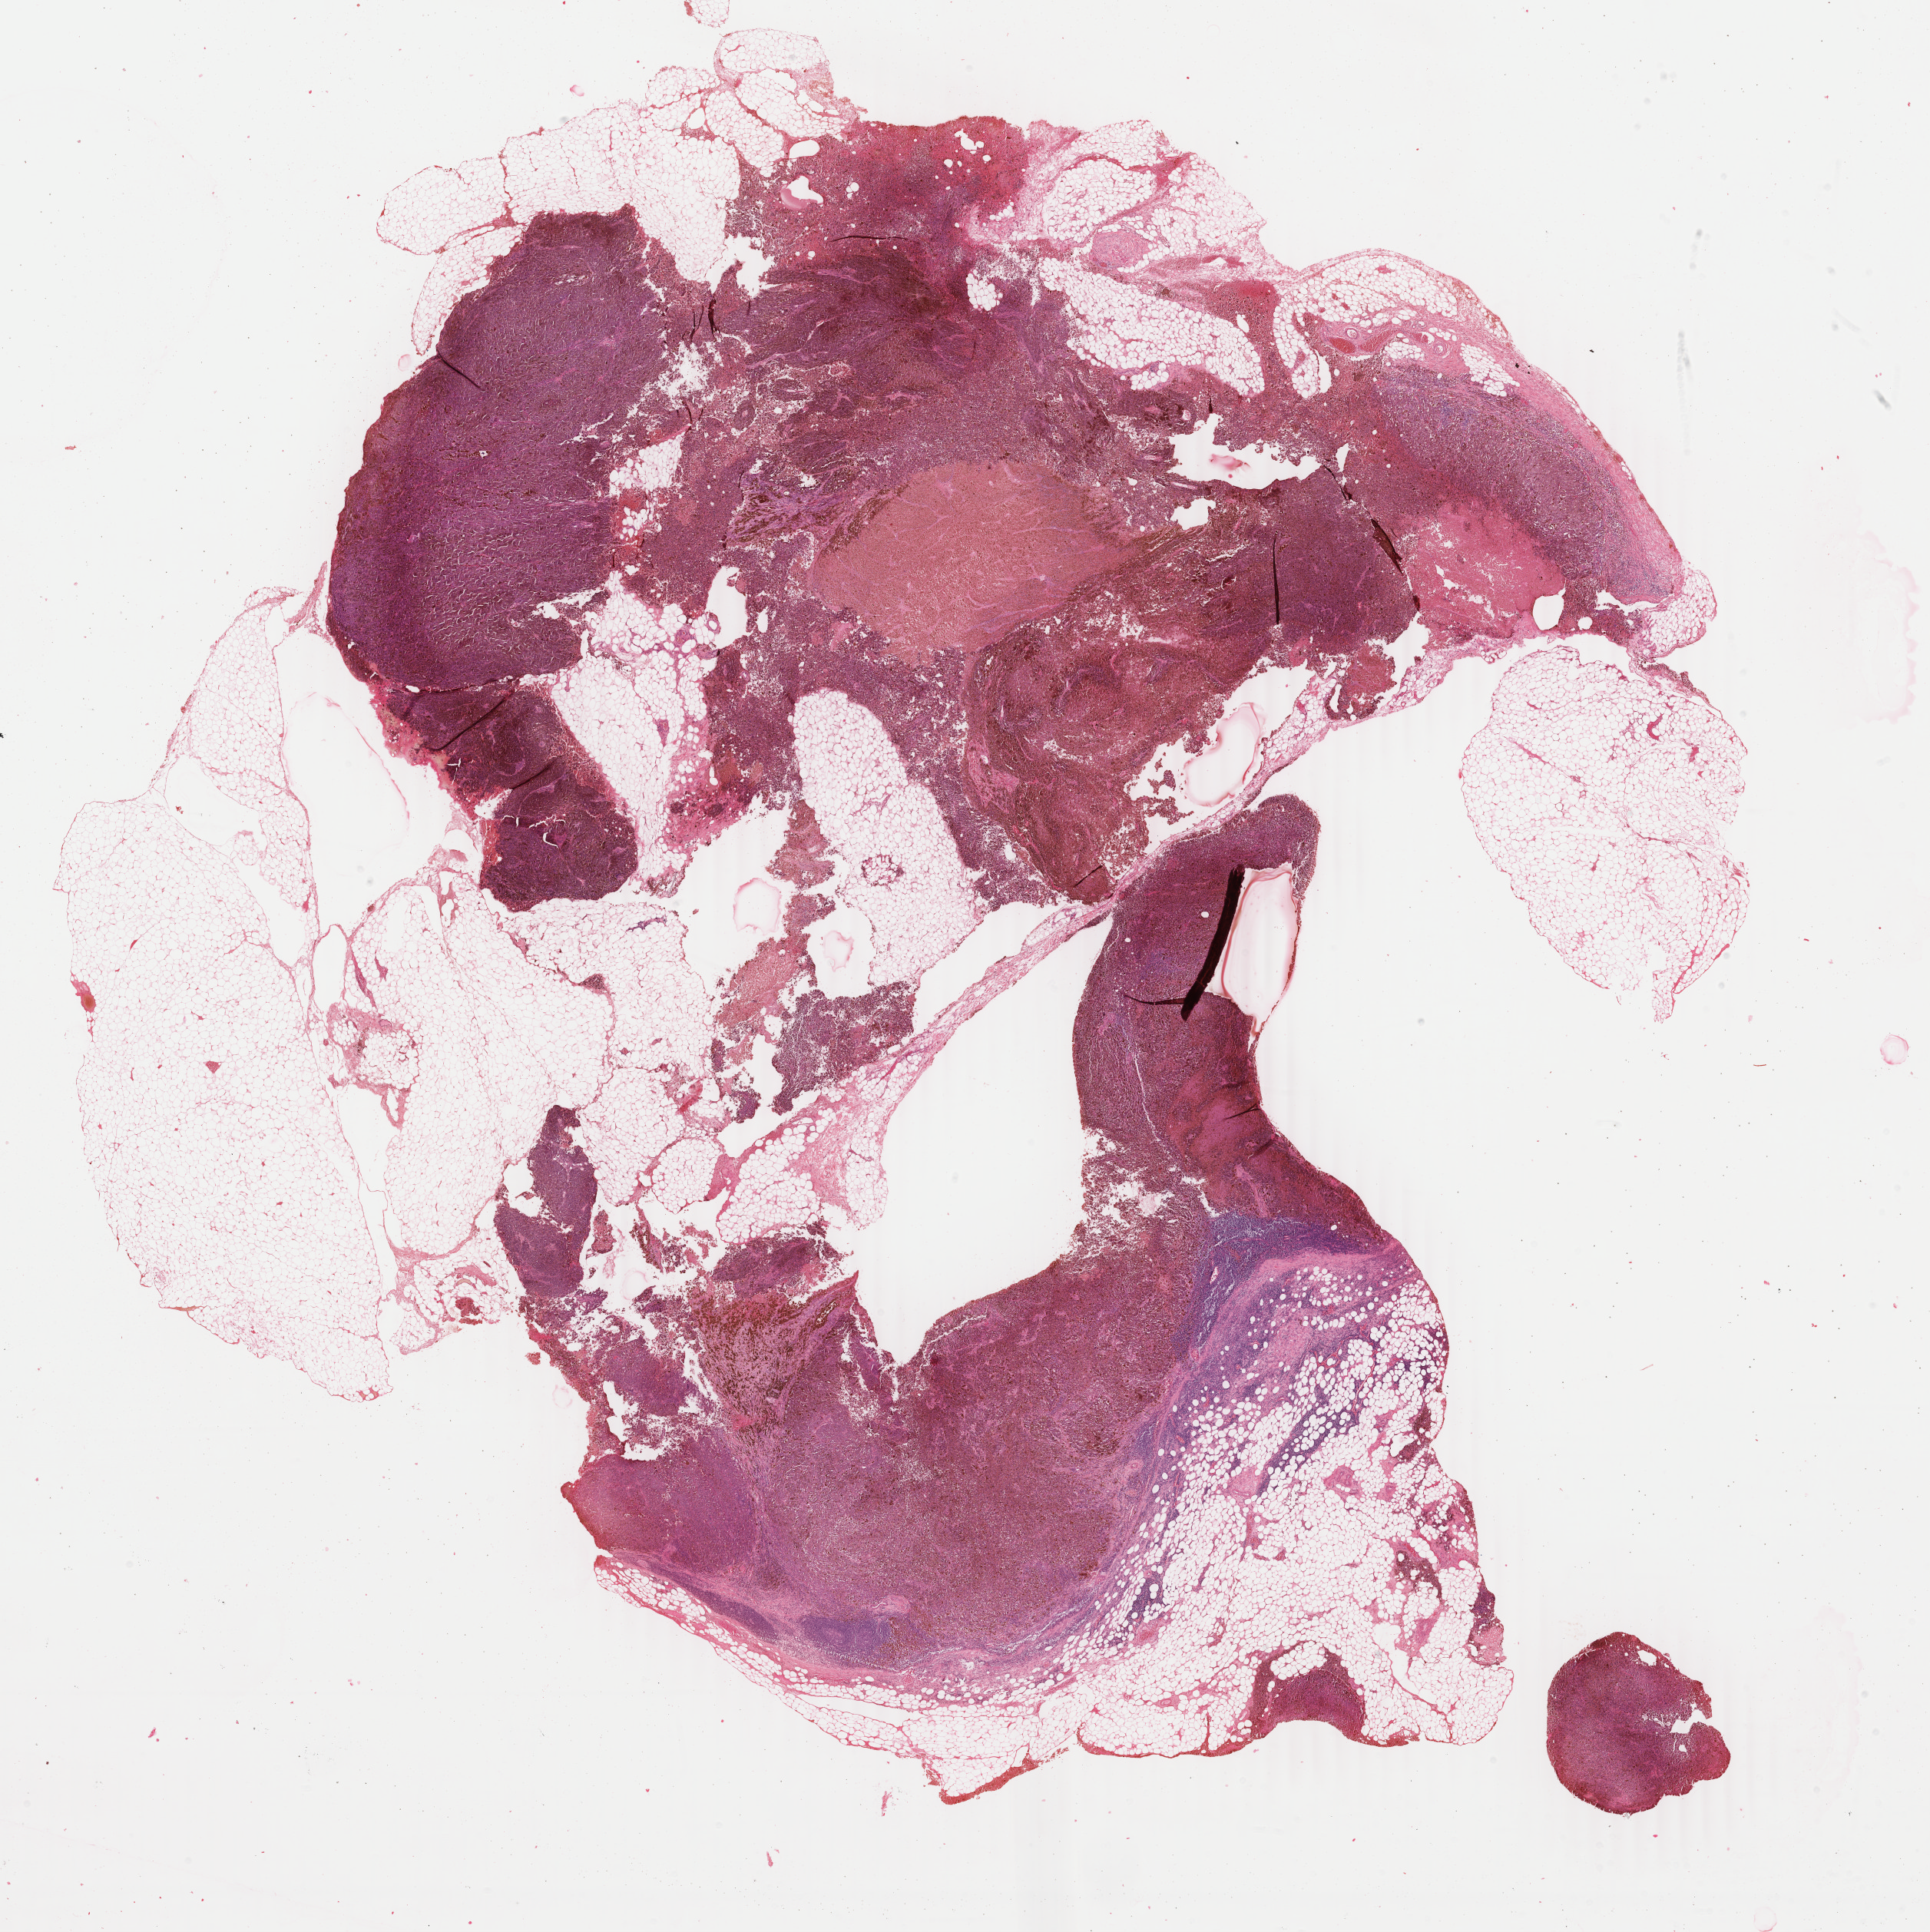
H&E-stained whole-slide image, whole scanned area (about 20.0 x 20.0 mm) shown as a low-resolution overview, formalin-fixed paraffin-embedded (FFPE) diagnostic section, primary tumour sample from the skin. Patient: male, age at initial diagnosis 54 years.
* histologic diagnosis: Malignant melanoma, NOS